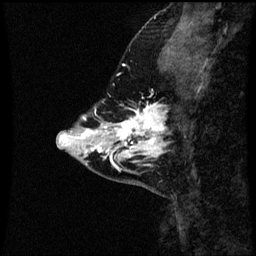
Breast MRI (dynamic contrast-enhanced), one sagittal slice; slice 16 of 60 in the series (ordered by position); dynamic contrast-enhanced series, image 2 of 3 at this slice position (ordered by acquisition); 1.5 T; TE 4.2 ms, TR 8.9 ms; 2 mm slice thickness; 256 × 256 image matrix, field of view 200 × 200 mm. Female patient, age 43 years. From the clinical record (not read from this slice): setting: breast cancer imaged before/during neoadjuvant chemotherapy; receptor status: HR-positive, HER2-negative.
Structures marked on this image (semi-automatically segmented with operator editing):
- analysis volume of interest (the breast-tissue region the enhancement analysis was run in; not a lesion): bounding box [x1, y1, x2, y2] px = [110, 102, 168, 163]
- tumour enhancement mask (voxels above the 70 % enhancement threshold inside the analysis volume of interest): [110, 104, 165, 163]